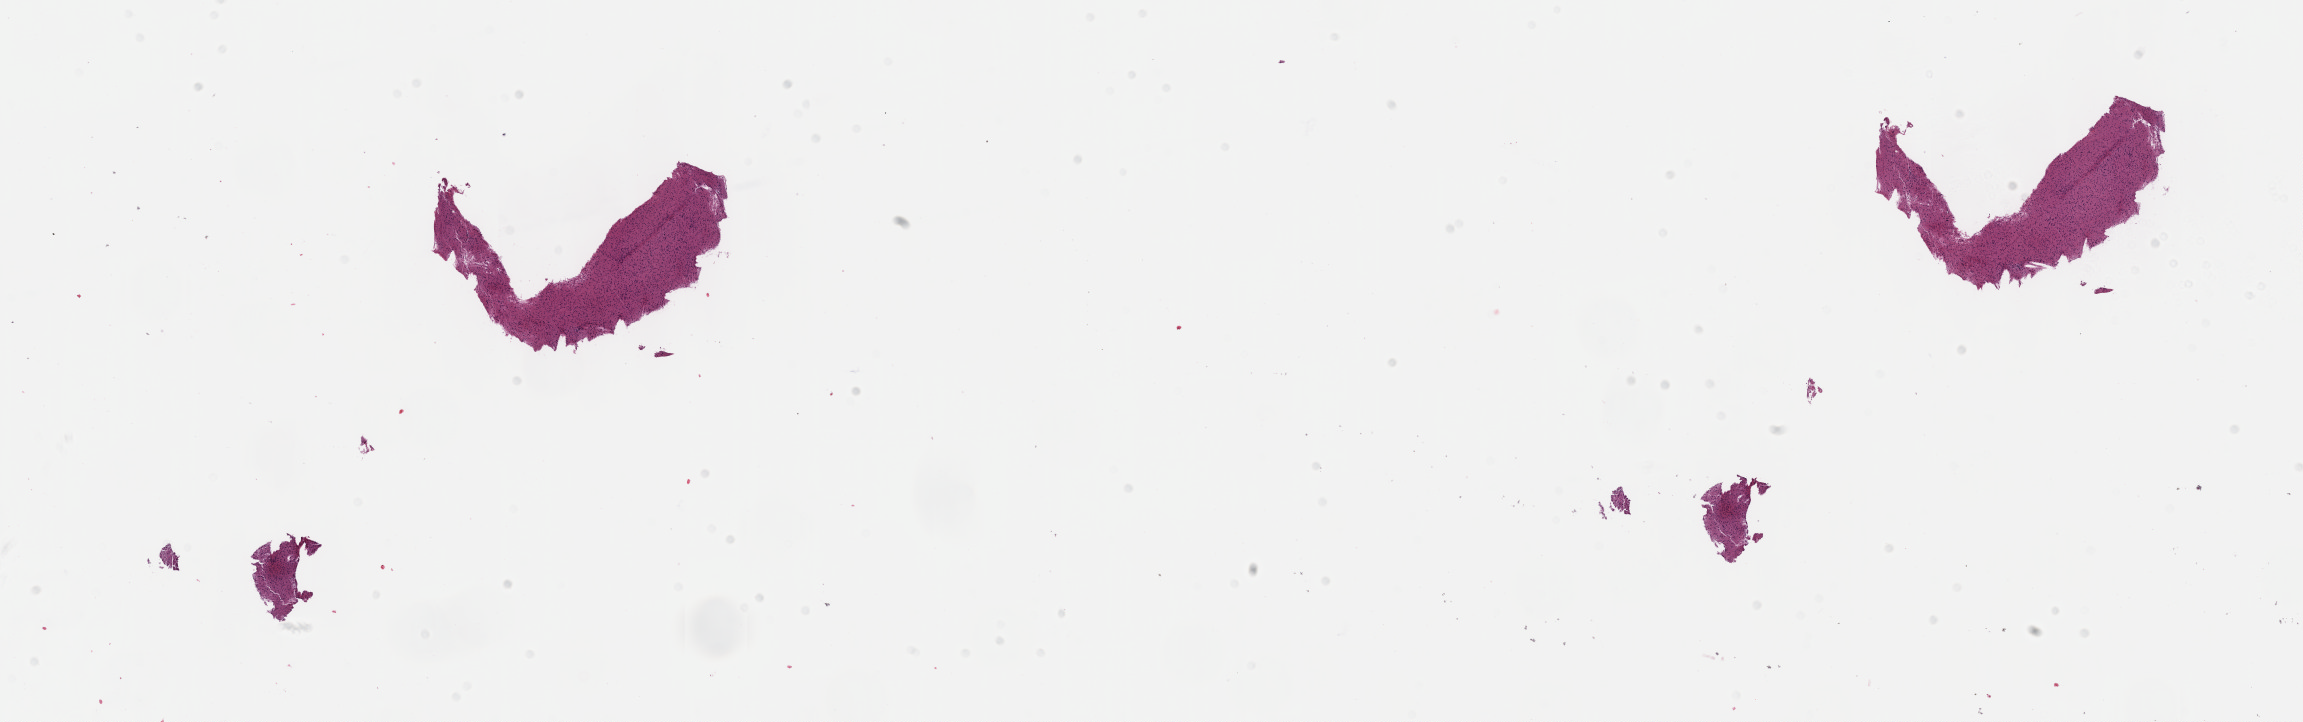
Digitized Hematoxylin and eosin (H&E) stained tissue section (whole slide) — low-resolution overview of the scanned area, about 18.6 x 5.8 mm (slide scanned at 40x); formalin-fixed paraffin-embedded (FFPE) diagnostic section; primary tumour sample from the brain. Patient: male, age at initial diagnosis 28 years. Histologic grade: G2 (moderately differentiated).
Histologic diagnosis: Mixed glioma.